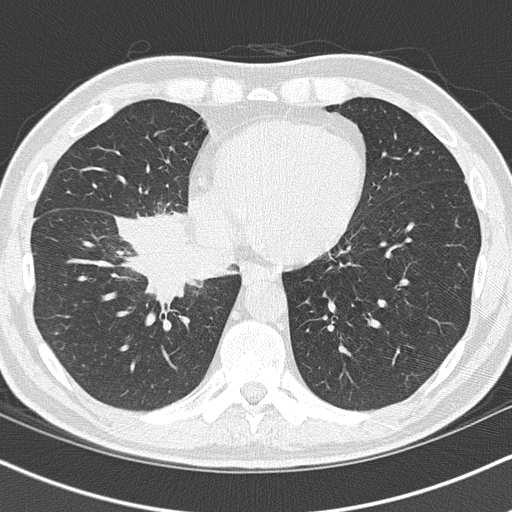
Low-dose screening chest CT, one axial slice. Position 42 of 151 along the scan axis. Reconstruction kernel B50f. 120 kVp. Lung window (W 1500 / L -600 HU). 2 mm slice thickness. 512 × 512 image matrix.
Annotated regions visible in this slice (outlined manually by an expert reader):
- lesion 1 (tumor, hilum of right lung): bounding box <122,211,190,302> (left, top, right, bottom; pixels)